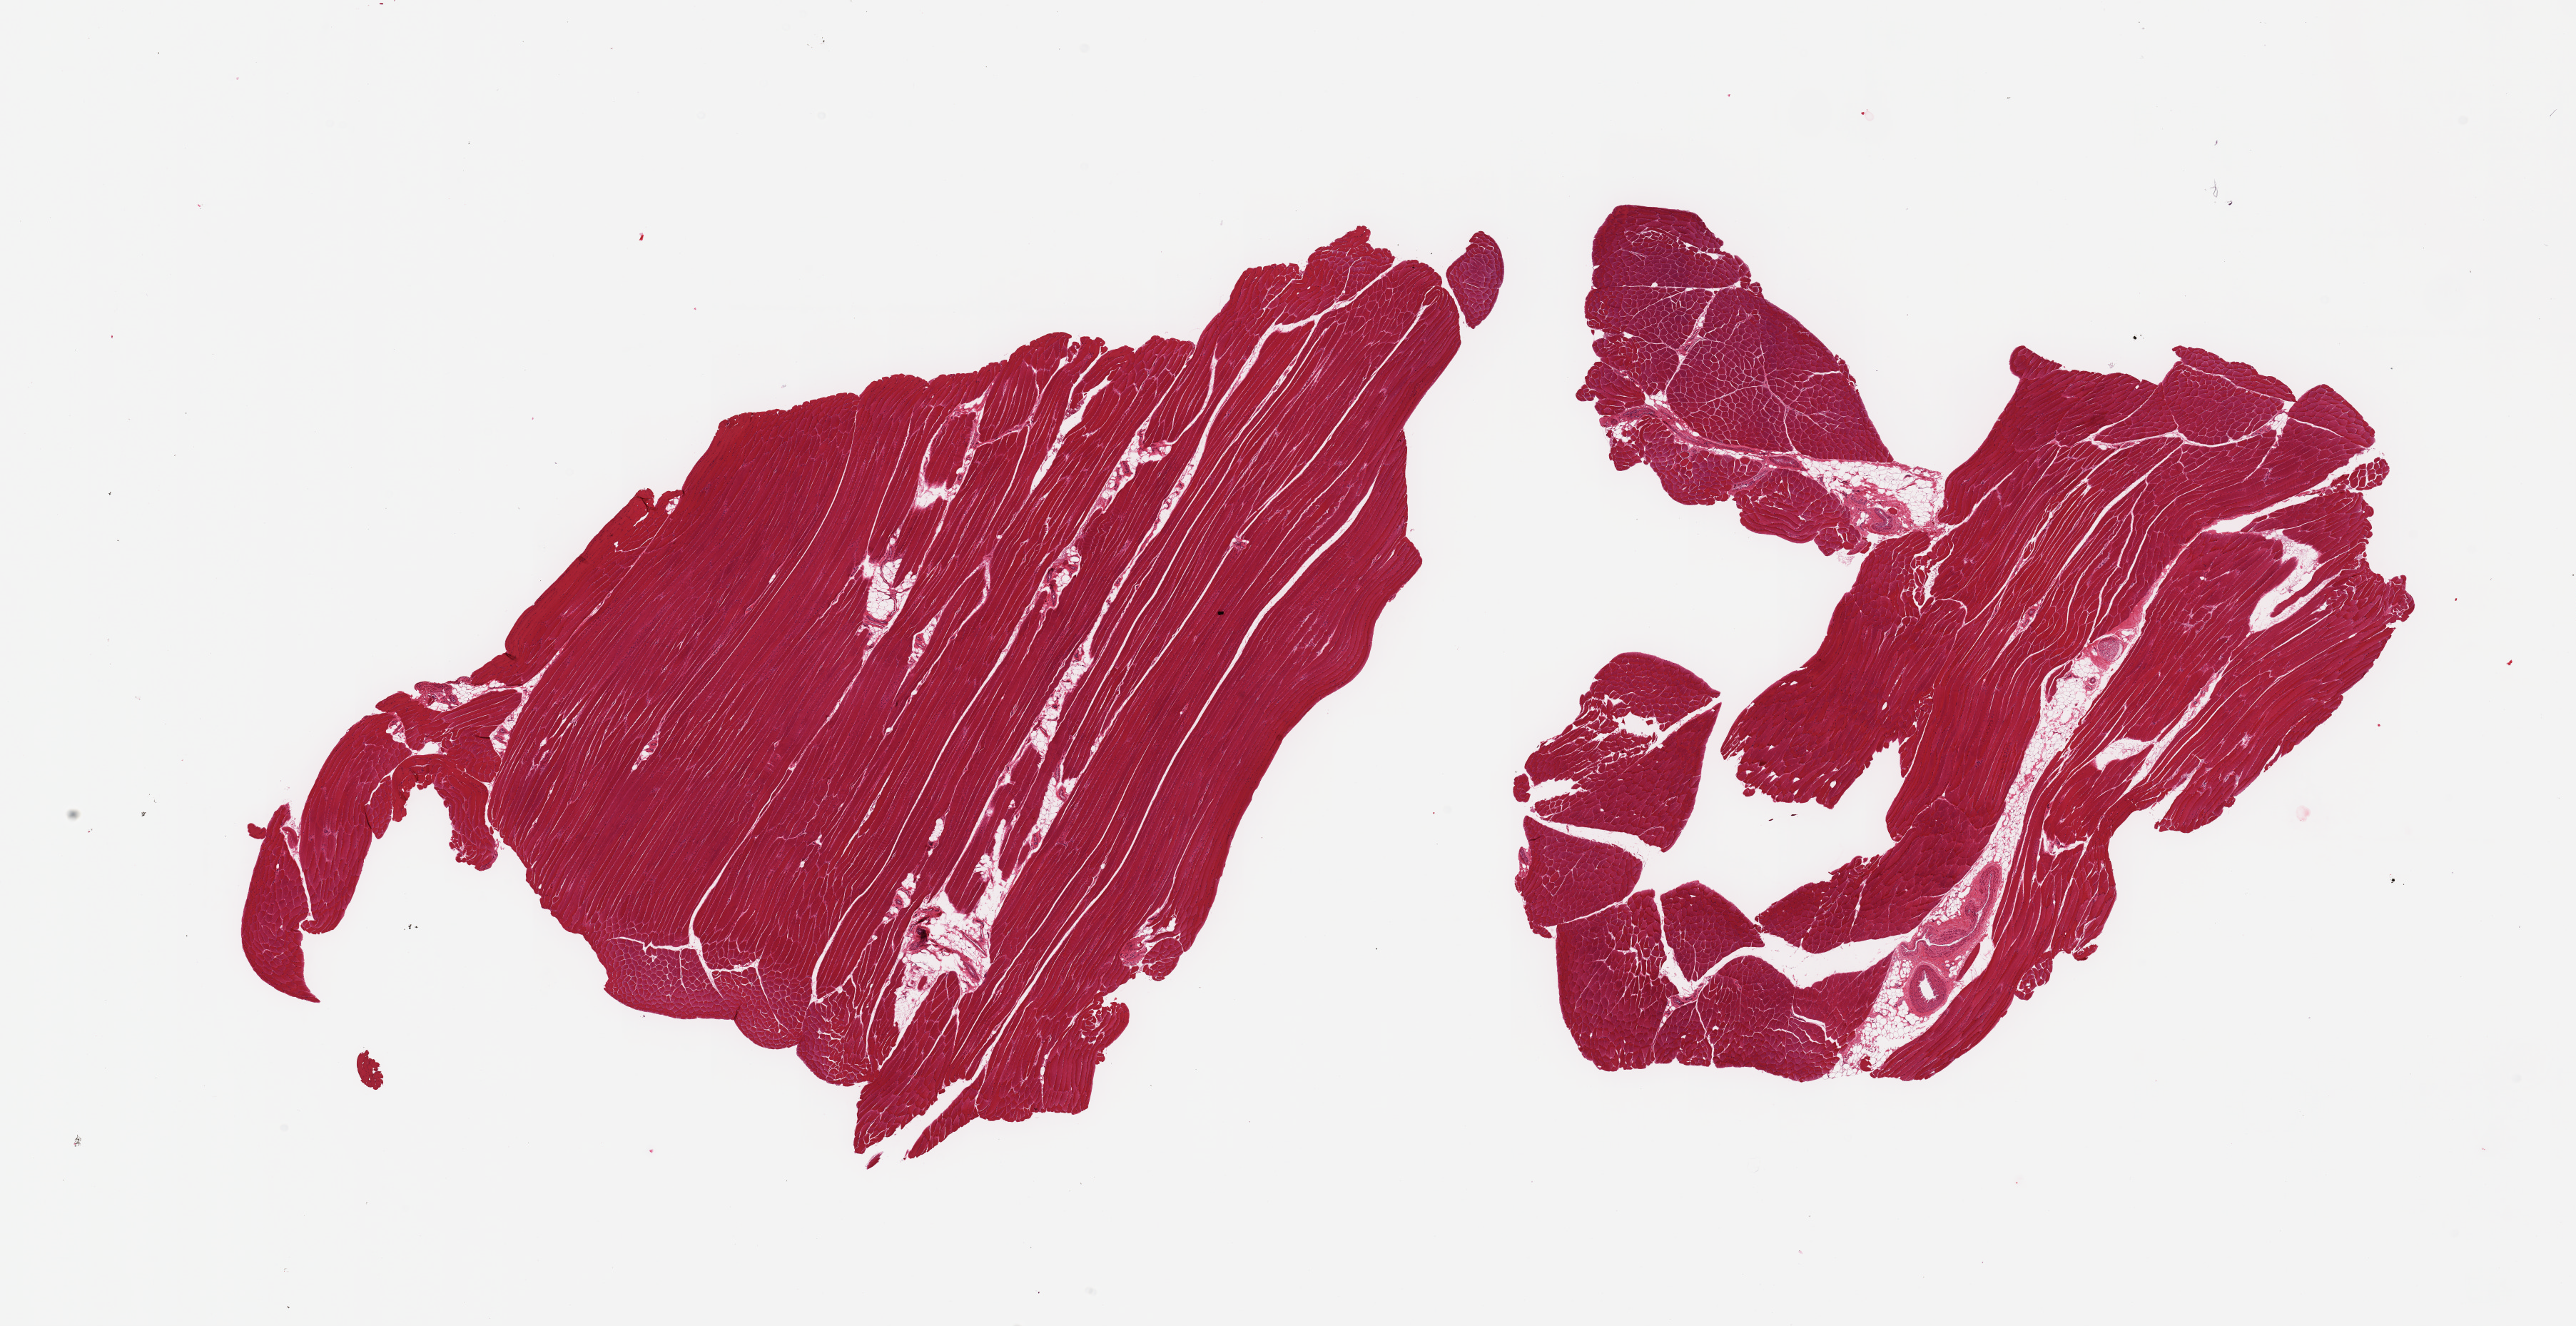
Digitized haematoxylin and eosin-stained section — shown as a low-resolution overview of the whole scanned area (about 28.5 x 14.7 mm, acquisition: 20x scan), PAXgene-fixed, paraffin-embedded tissue, sampled site (target tissue): skeletal muscle, tissue donor sample. Female donor.
Review note (as recorded): 2 pieces; up to 10% internall fat.